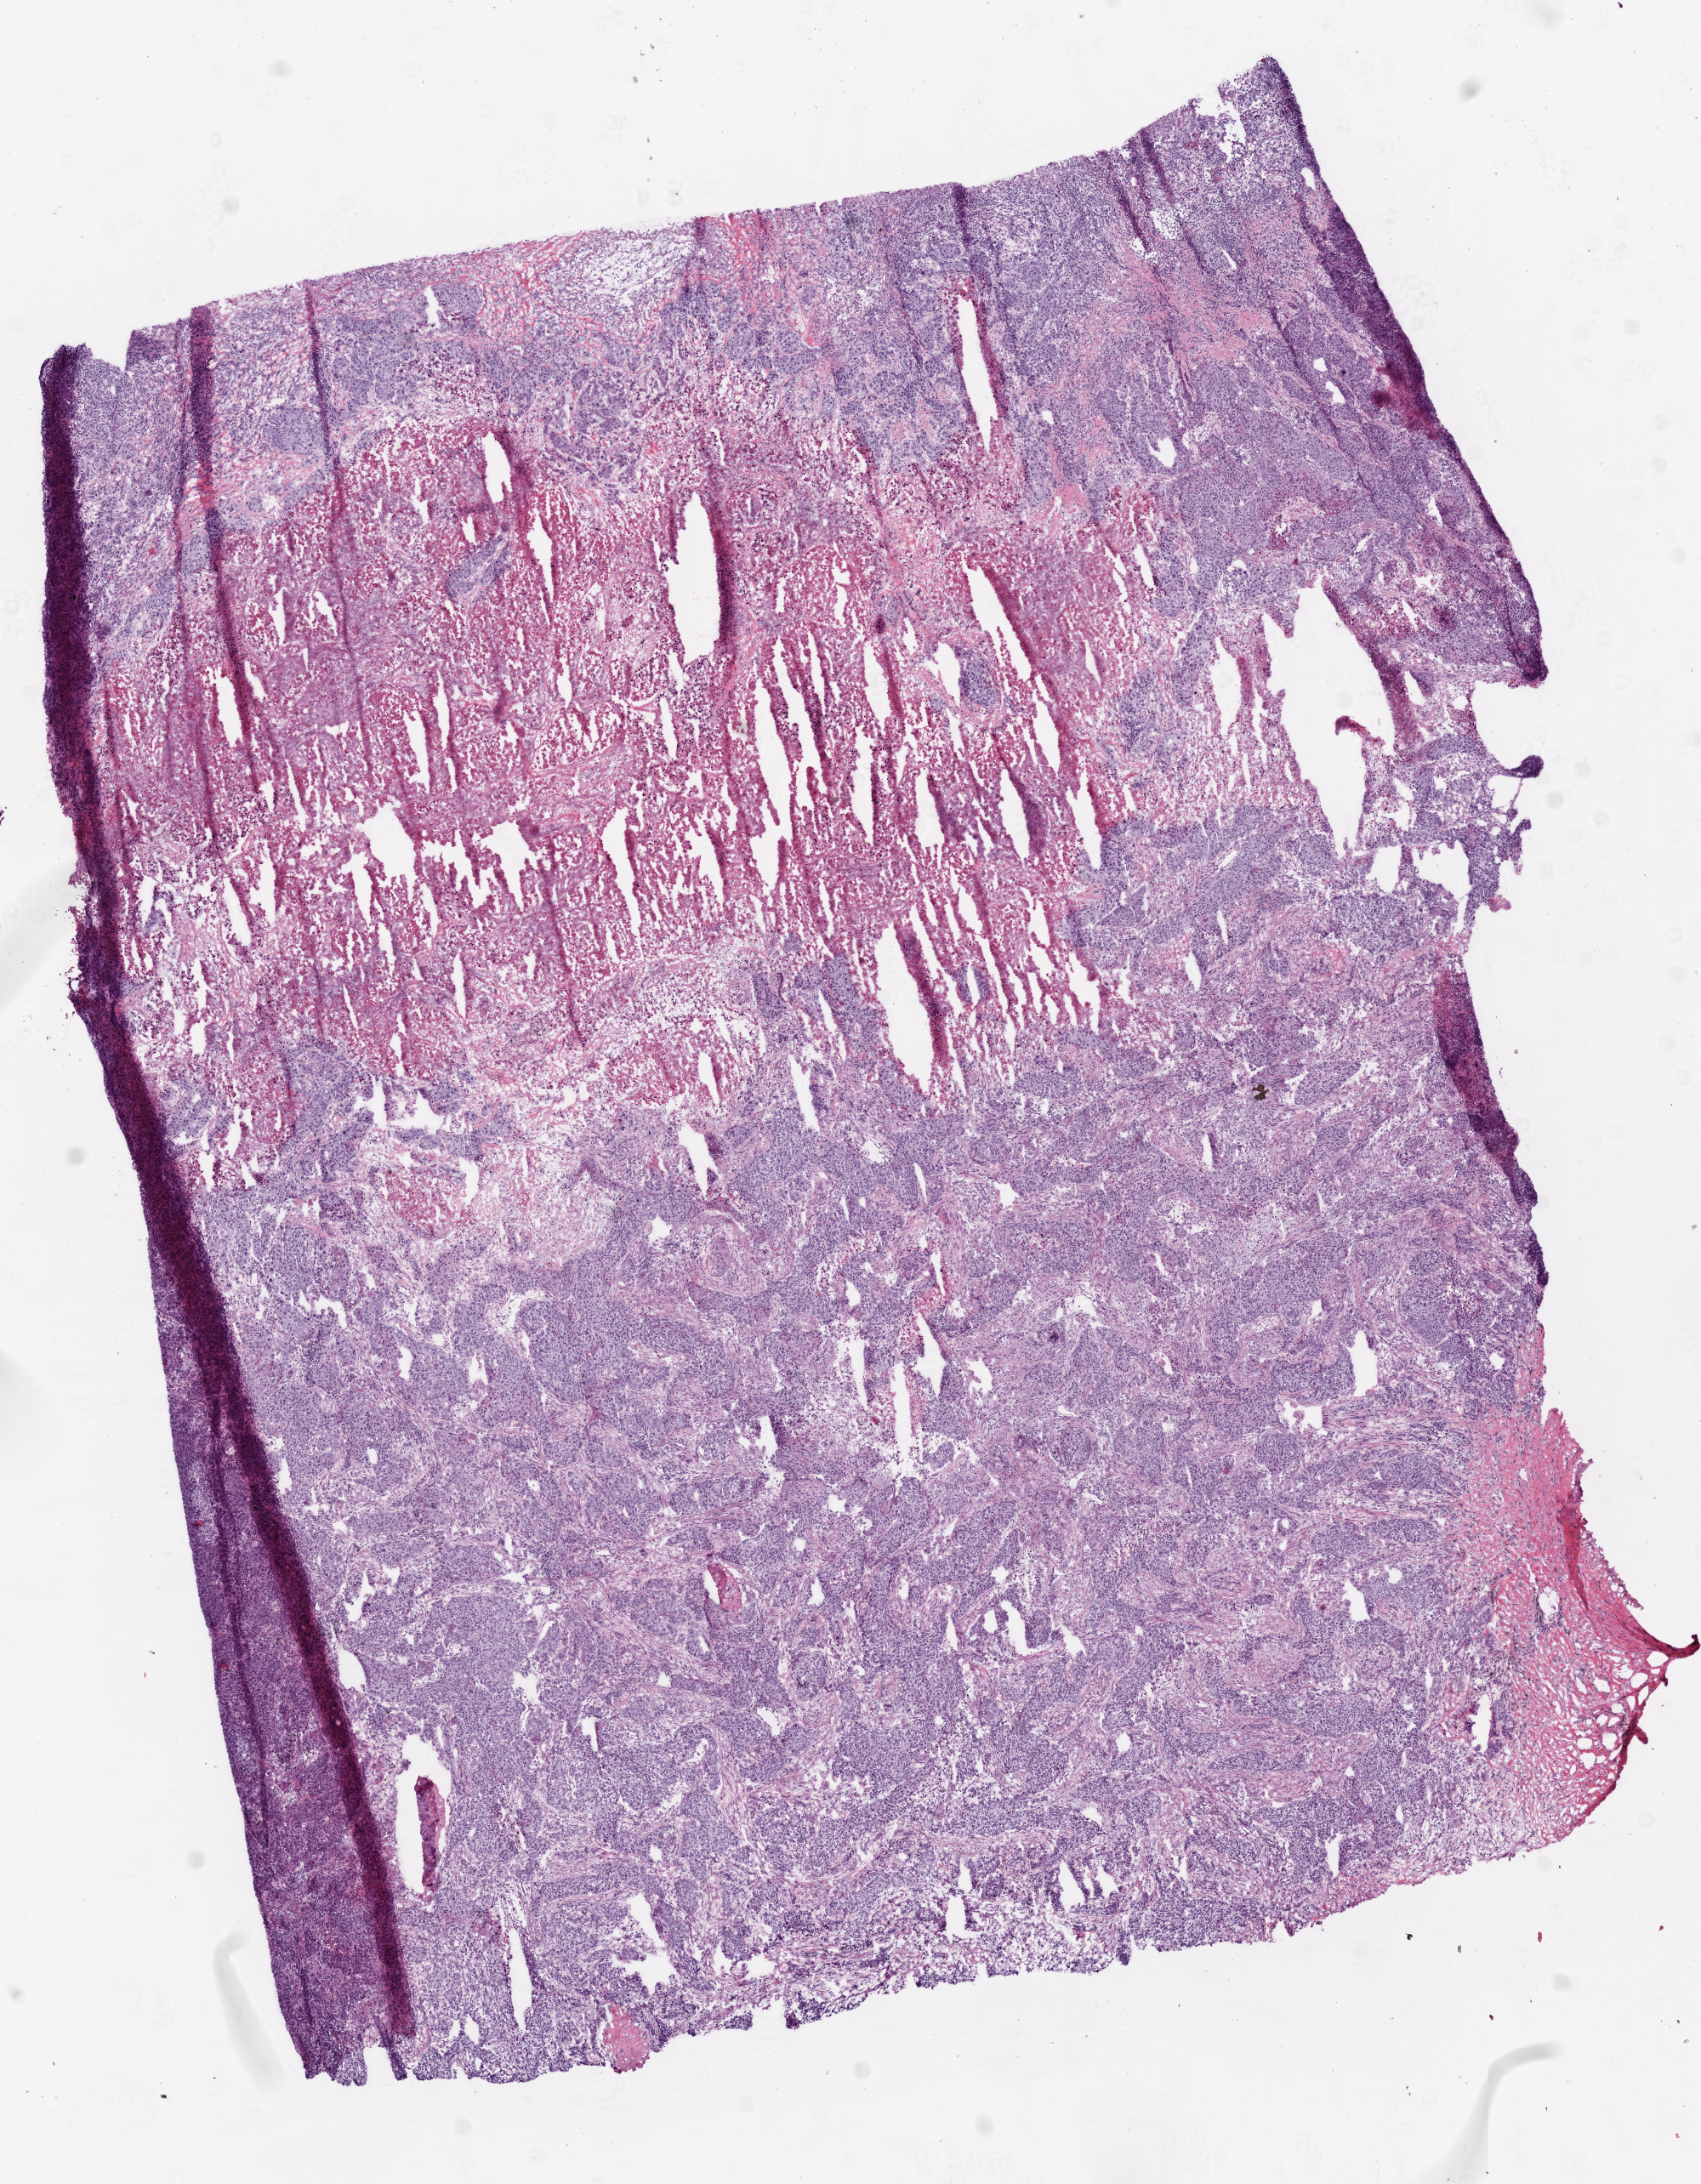
Whole-slide histology image, H&E-stained — shown as a low-resolution overview of the whole scanned area (about 8.0 x 10.3 mm, slide scanned at 20x), frozen section, lung, primary tumour sample. Patient: male, age at initial diagnosis 68 years. Slide review estimates, as recorded: tumour cells 57%, tumour nuclei 75%, normal cells 3%, stromal cells 10%, necrosis 30%.
AJCC pathologic stage: IIIB. Pathologic diagnosis: Squamous cell carcinoma, NOS (upper lobe, lung).